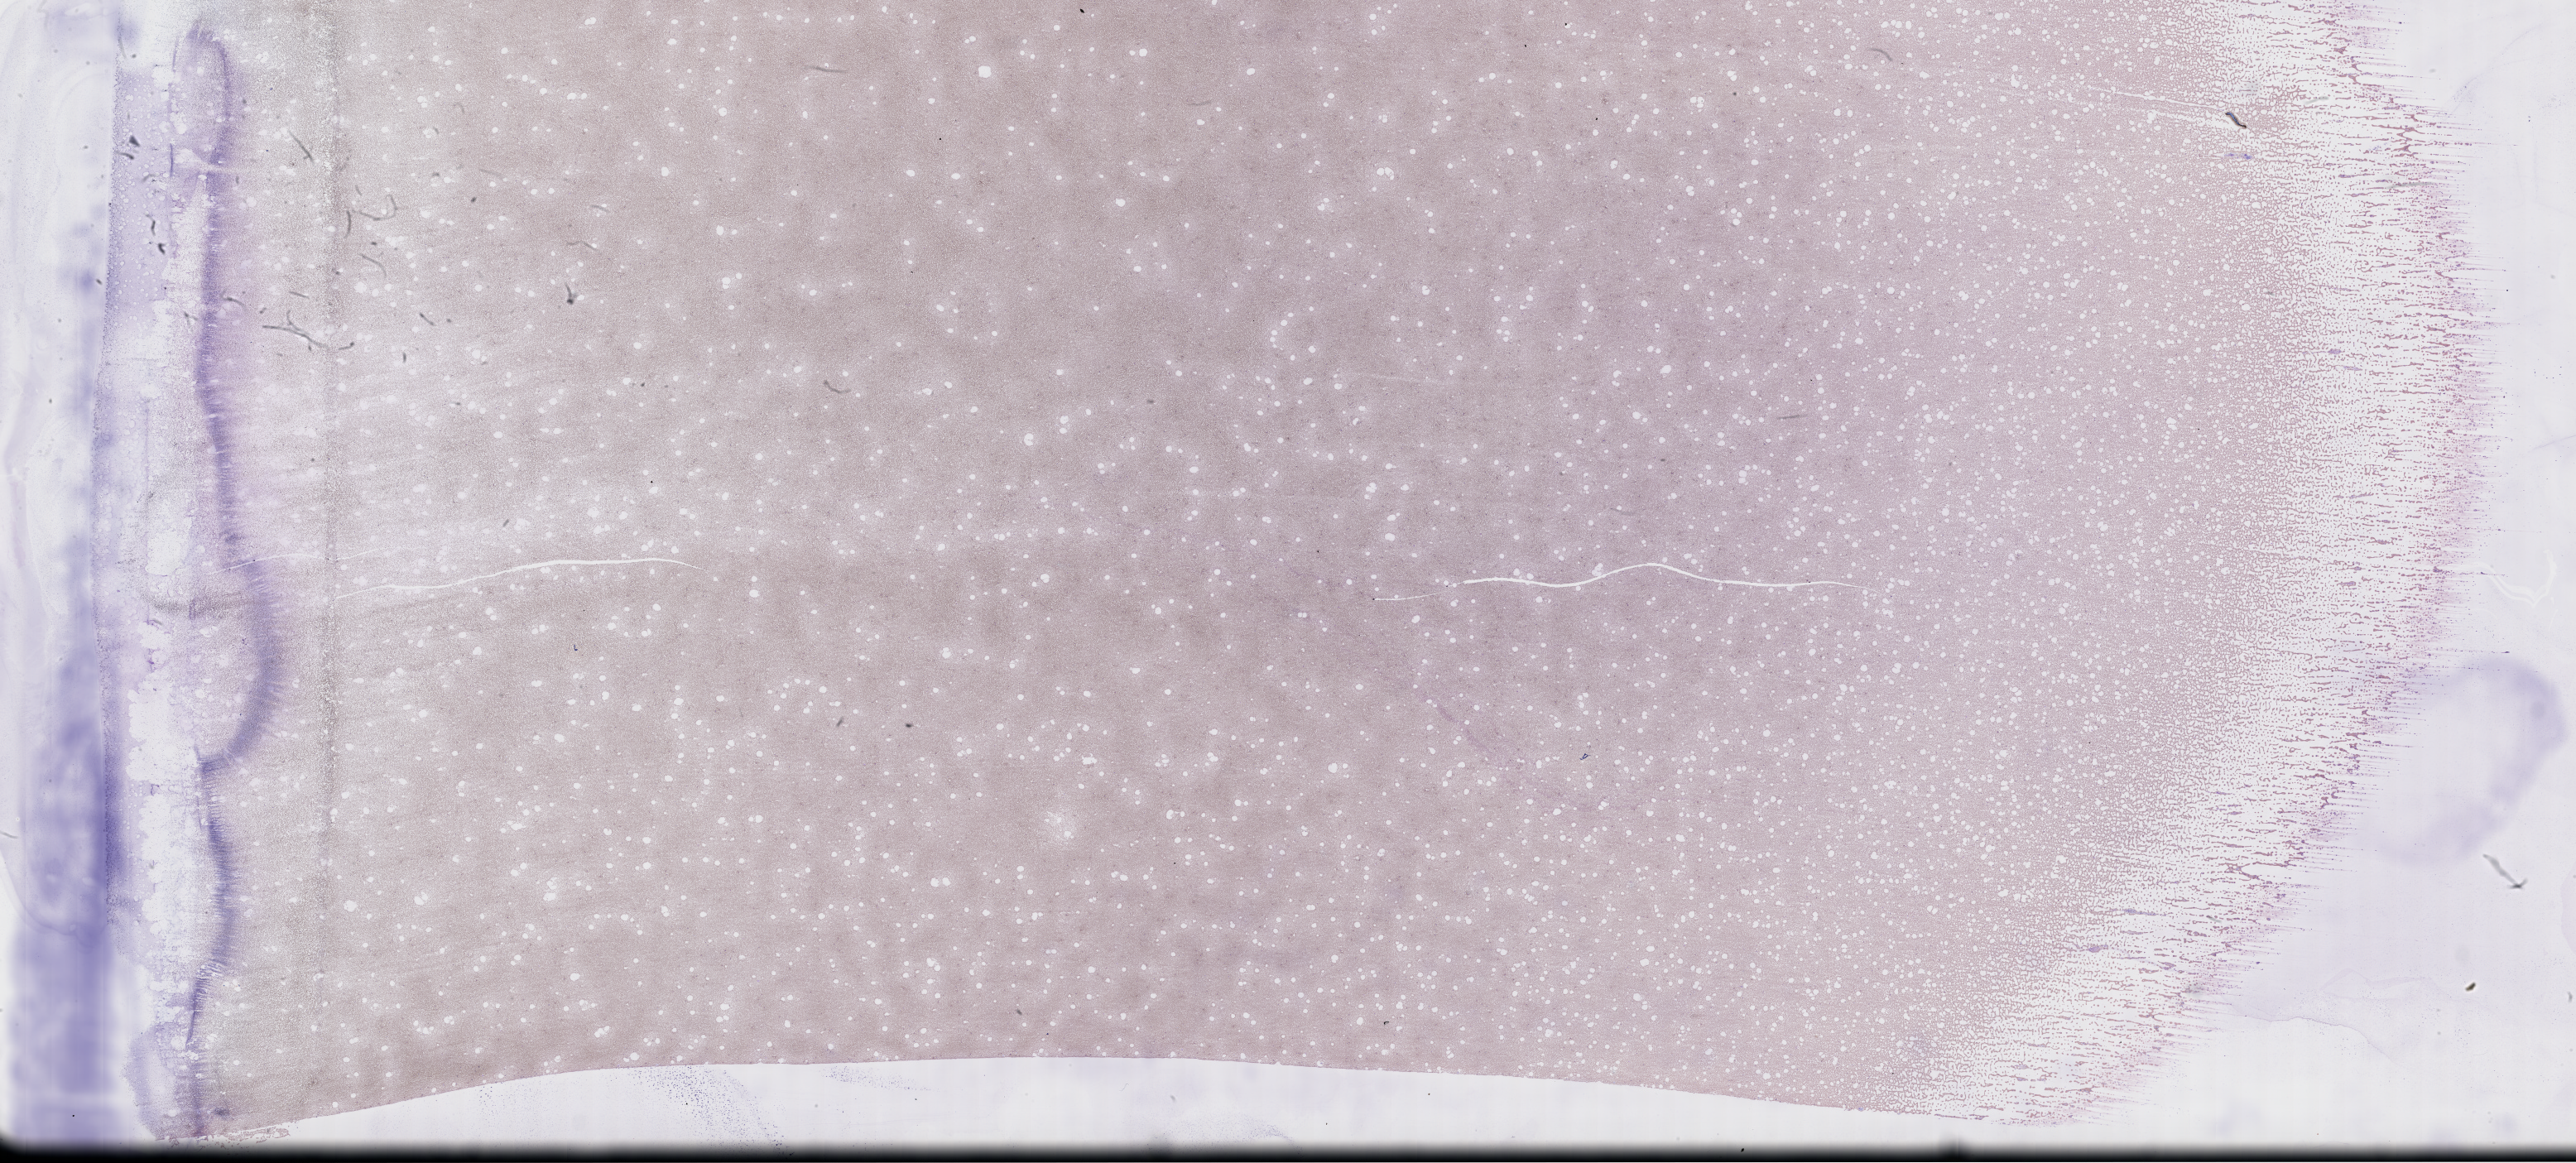
Whole-slide image of a whole blood smear, Wright-Giemsa stain — whole scanned area (about 50.3 x 22.7 mm) shown as a low-resolution overview; EDTA-anticoagulated smear; specimen time point: collected on treatment. Patient: male.
From a patient with: Plasma Cell Myeloma.